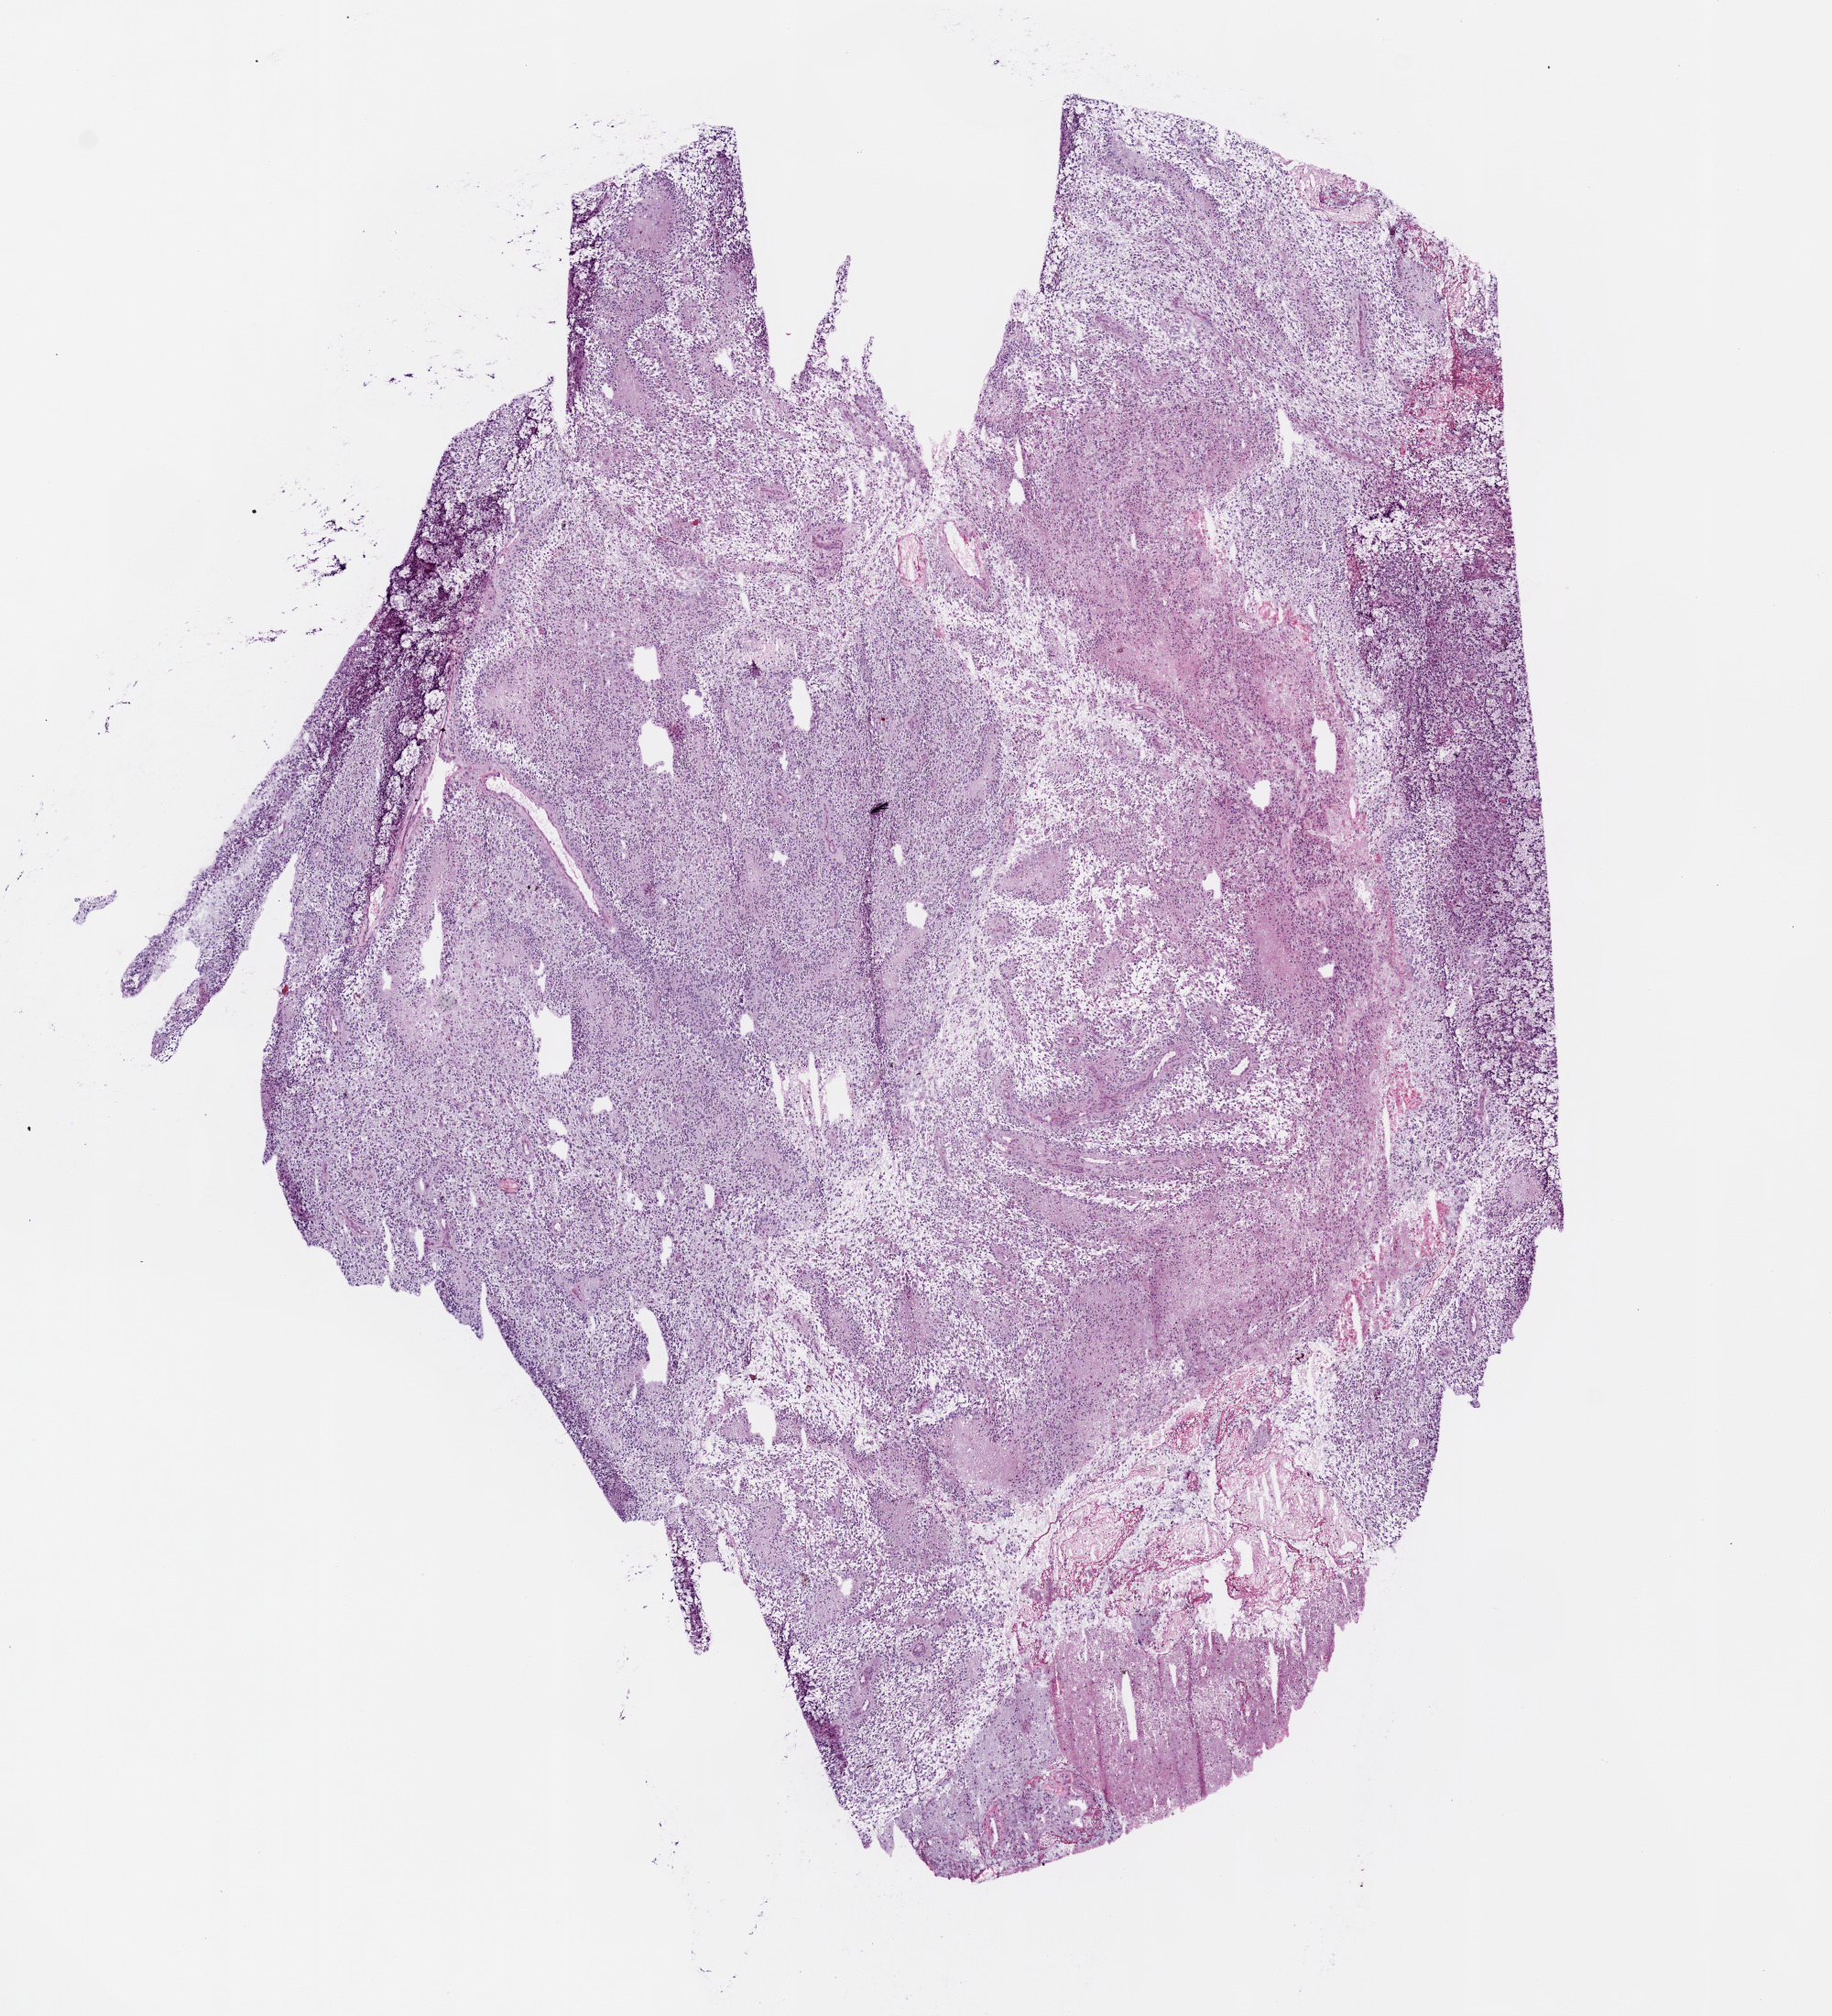
H&E-stained whole-slide image — shown as a low-resolution overview of the whole scanned area (about 8.0 x 8.8 mm, slide scanned at 20x). Frozen section. Brain, primary tumour sample. Male patient; age at initial diagnosis 75 years. Composition of this section per pathologist review: tumour cells 60%, tumour nuclei 80%, normal cells 0%, stromal cells 0%, necrosis 40%.
Pathologic diagnosis: Glioblastoma.